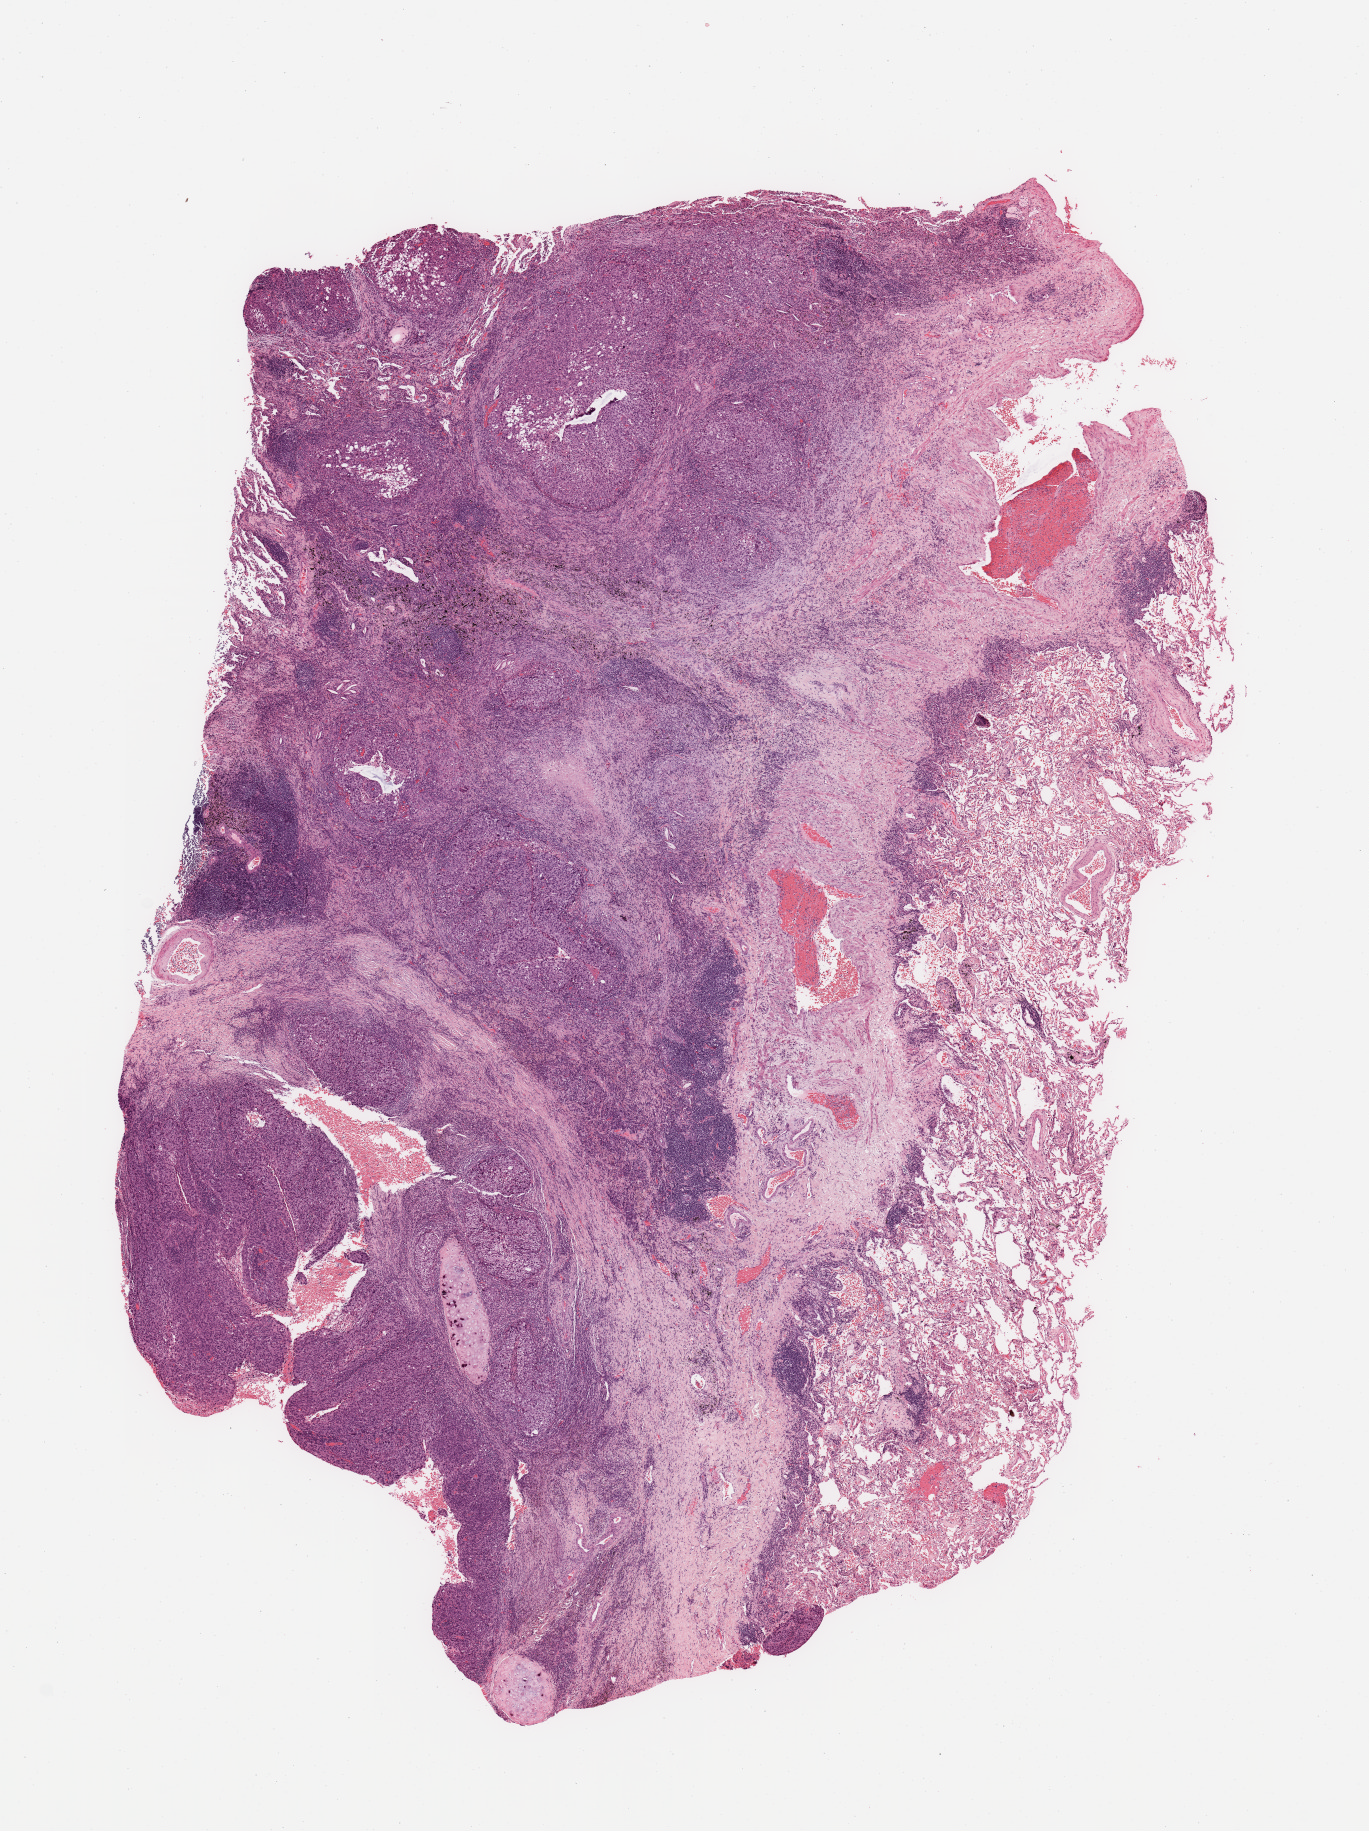
Digitized H&E tissue section (whole slide) — shown as a low-resolution overview of the whole scanned area (about 10.8 x 14.5 mm, acquisition: 20x scan), lung, tumour tissue. 76-year-old male patient. Histologic grade: G2 (moderately differentiated).
* primary tumour site (as recorded): left upper lobe
* diagnosis: Squamous cell carcinoma, NOS
* AJCC pathologic stage: IA3